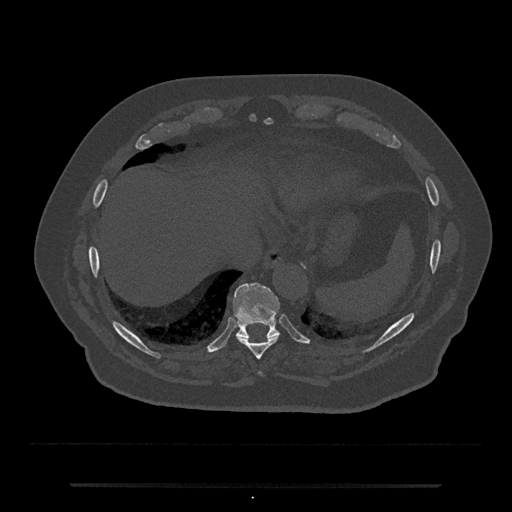
CT including the spine, one axial slice. Position 736 of 797 along the scan axis. 120 kVp. Bone window (W 1800 / L 400 HU). 512 × 512 image matrix, field of view 434 × 434 mm. Male patient, age 80 years. From the clinical record (not read from this slice): primary cancer: prostate.
Annotated regions visible in this slice (semi-automatically segmented with operator editing):
- T10 vertebra: bounding box (x1, y1, x2, y2) in pixels: (233, 283, 280, 338)
- T9 vertebra: (237, 335, 279, 360)